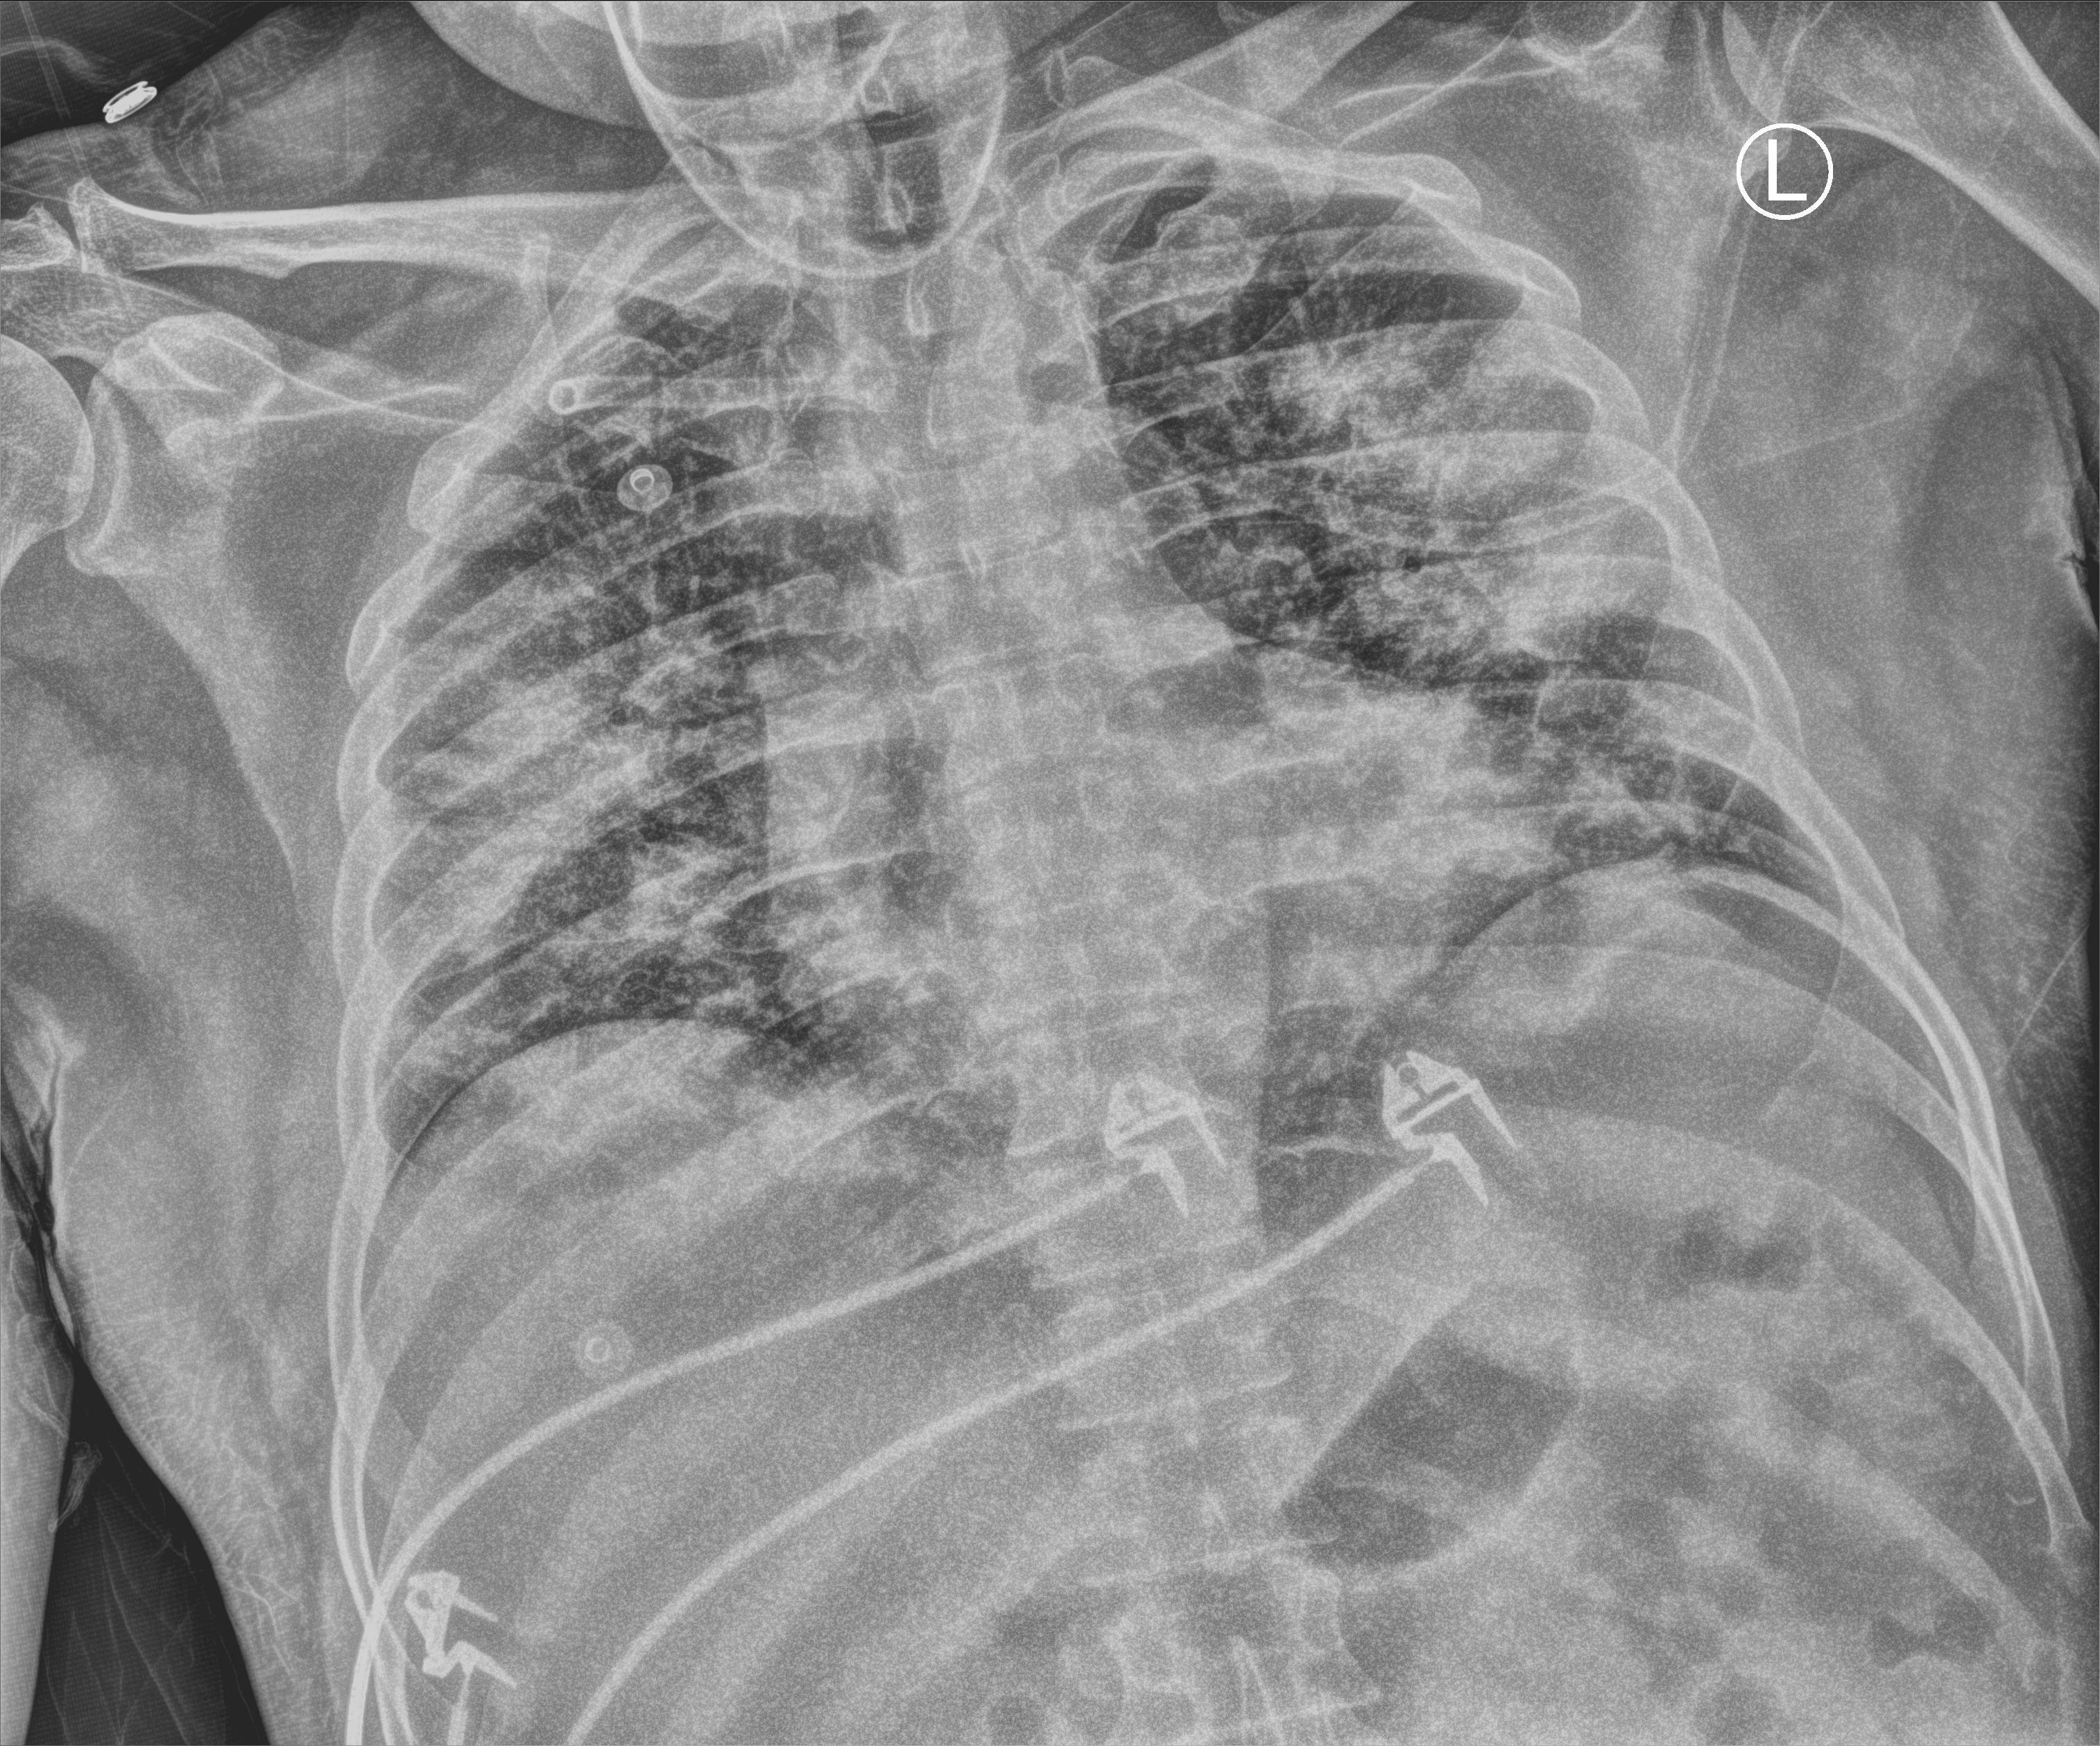
Chest X-ray (portable); anteroposterior (AP) projection. Male patient hospitalised with COVID-19, age 18–59 years.
Admission-level facts for this patient (not findings on this image; timing relative to this image not recorded):
- admitted to intensive care during this hospital stay: yes
- other chronic lung disease (admission record): no